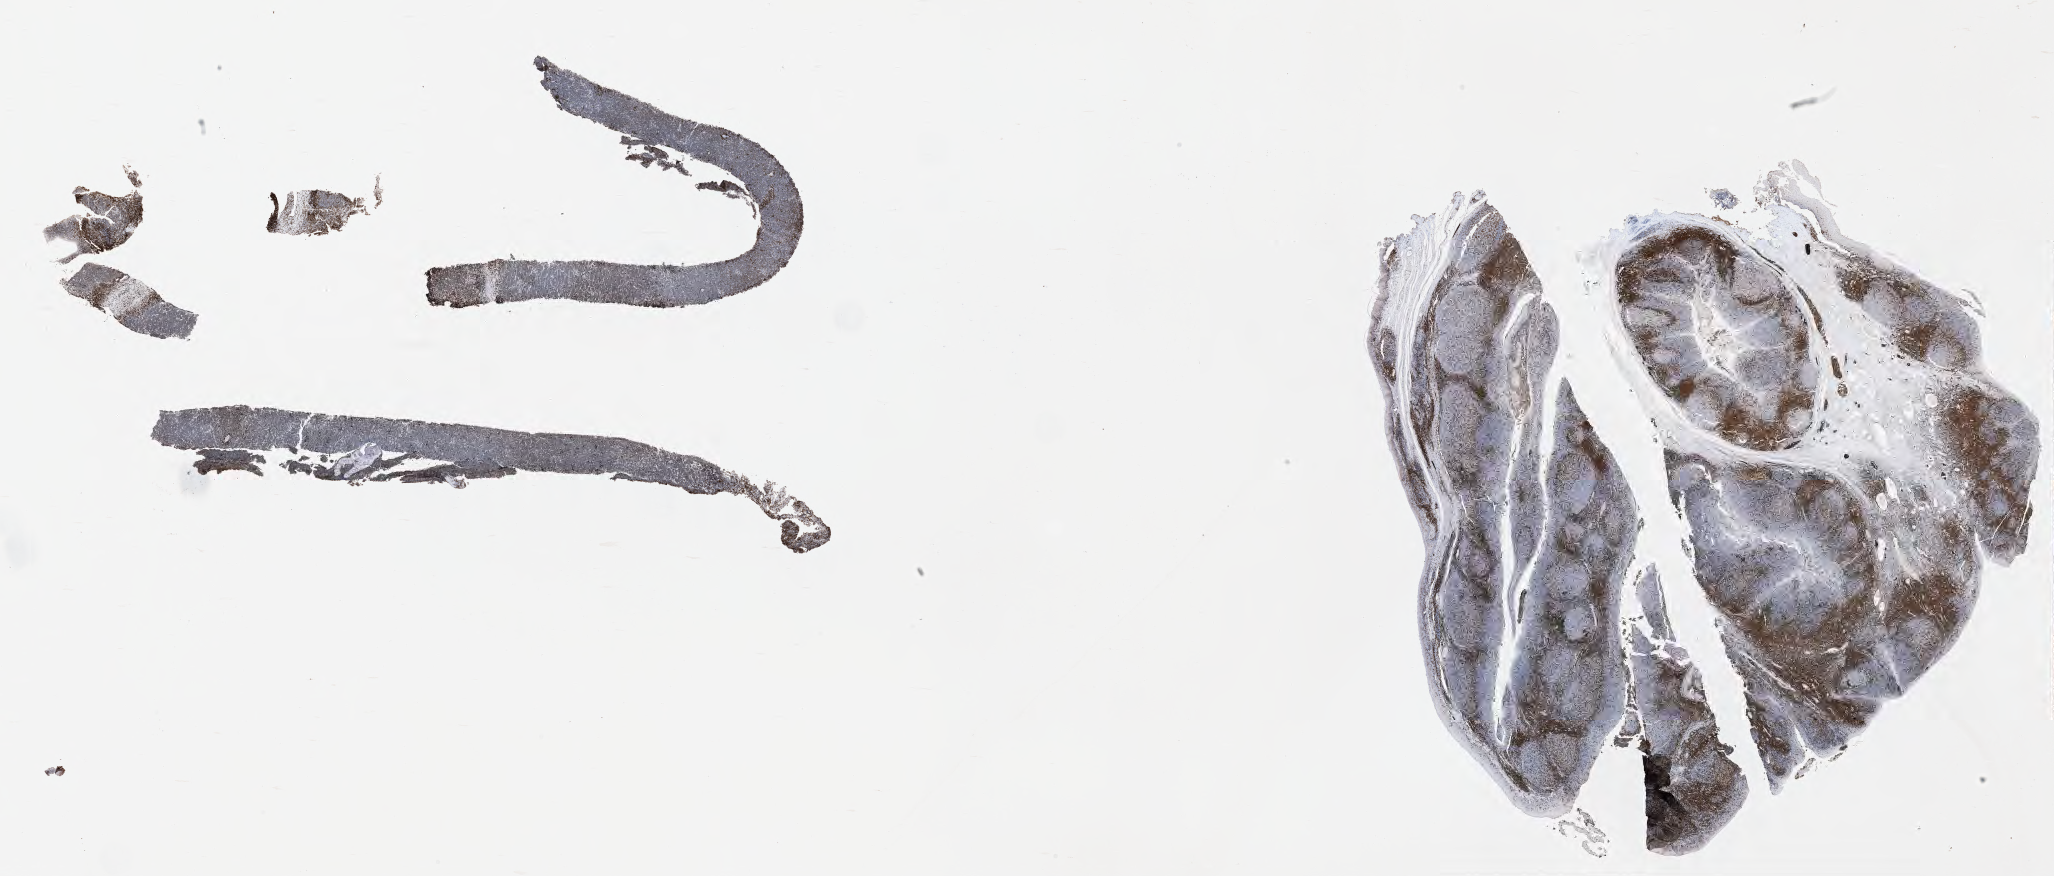
IHC for CD3, whole-slide image, whole scanned area (about 33.2 x 14.2 mm) shown as a low-resolution overview; specimen: tumor tissue. Patient male; 55 years old.
Histologic diagnosis: Burkitt lymphoma, NOS.